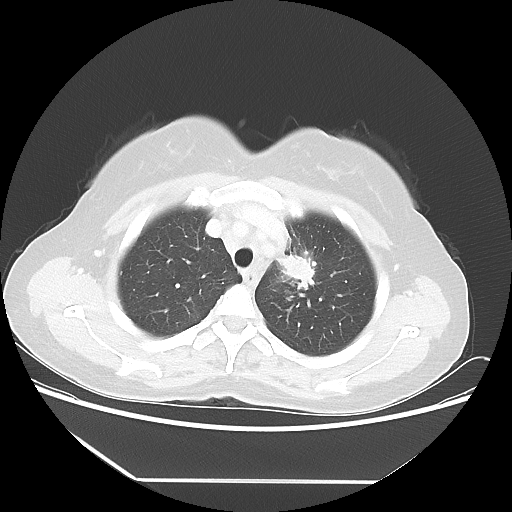
Chest CT, one axial slice; reconstruction kernel LUNG; 100 kVp; lung window (W 1500 / L -600 HU); 5 mm slice thickness; 512 × 512 image matrix, field of view 390 × 390 mm. Female patient, age 50 years. Case-level facts recorded for this patient, not image findings: clinical TNM (as recorded): T2 N3 M0.
Outlined on this slice (rectangle marked by the reading radiologist):
- lung tumour (recorded histology: adenocarcinoma): bounding box (x1, y1, x2, y2) in pixels: (276, 241, 321, 287)